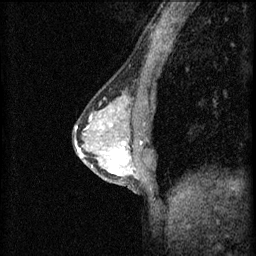
Breast MRI (dynamic contrast-enhanced), one sagittal slice; slice 28 of 60 in the series (ordered by position); 3 images stored at this slice position (order not interpretable as contrast timing); 1.5 T; TE 4.2 ms, TR 8.2 ms; 2 mm slice thickness; 256 × 256 image matrix. Female patient, age 44 years.
Outlined on this slice (semi-automatic segmentation, software-assisted and operator-edited):
- analysis volume of interest (the breast-tissue region the enhancement analysis was run in; not a lesion): bounding box (x1, y1, x2, y2) in pixels: (102, 132, 151, 181)
- tumour enhancement mask (voxels above the 70 % enhancement threshold inside the analysis volume of interest): (110, 142, 129, 175)